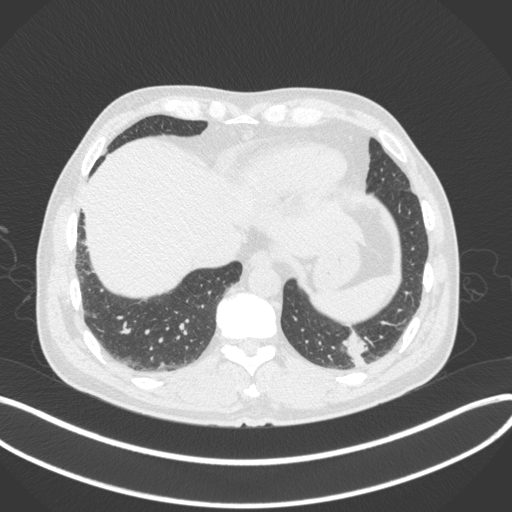
Chest CT, one axial slice. Position 56 of 313 along the scan axis. 120 kVp. Lung window (W 1500 / L -600 HU). 512 × 512 image matrix, field of view 400 × 400 mm. Male patient, age 54 years. From the clinical record (not read from this slice): clinical TNM (as recorded): T1c N0 M1.
Structures marked on this image (rectangle marked by the reading radiologist):
- lung tumour (recorded histology: adenocarcinoma): bounding box [x1, y1, x2, y2] px = [338, 325, 378, 366]